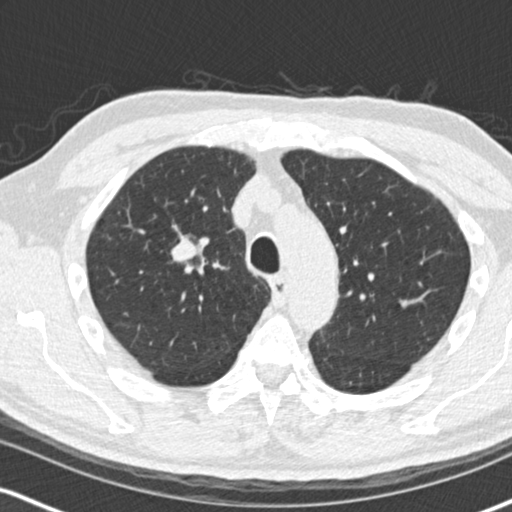
Low-dose screening chest CT, one axial slice; position 114 of 170 along the scan axis; 120 kVp; lung window (W 1500 / L -600 HU); 2 mm slice thickness; 512 × 512 image matrix, field of view 320 × 320 mm.
Annotated regions visible in this slice (expert manual segmentation):
- lesion 1 (tumor, upper lobe of right lung): box from (x=171, y=237) to (x=200, y=263) px